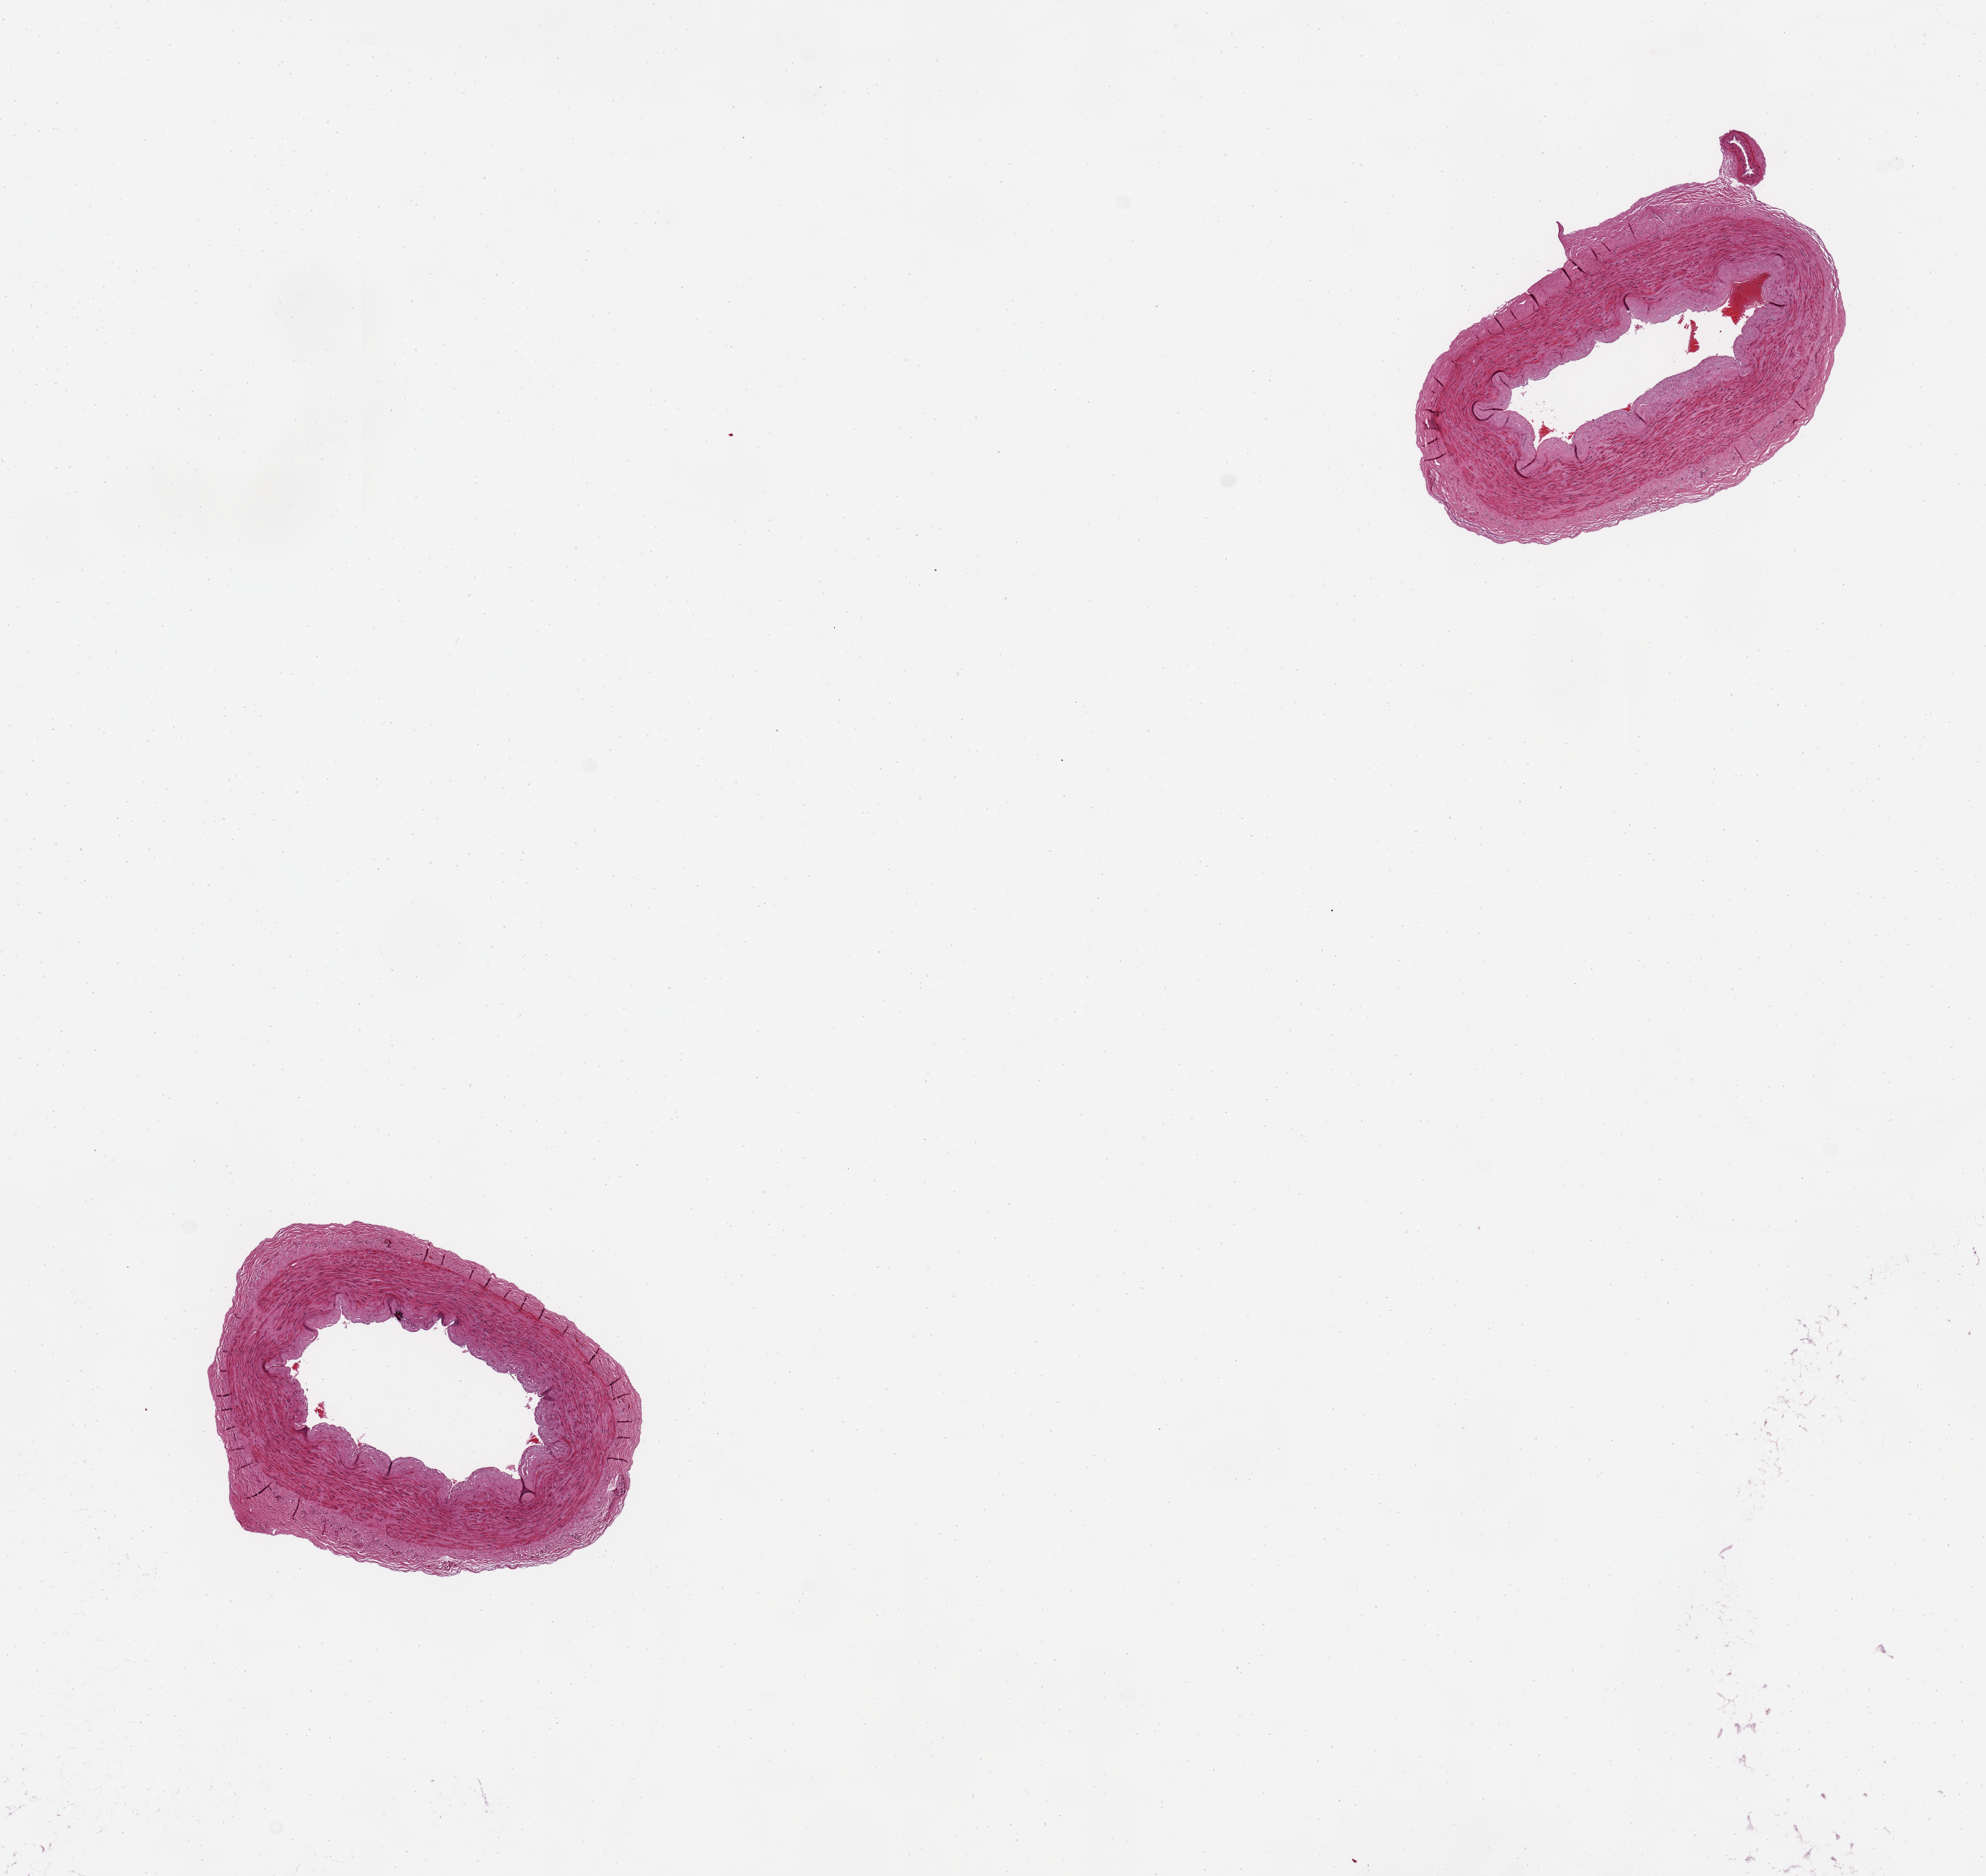
Whole-slide image, haematoxylin and eosin stain, brightfield, low-resolution overview of the scanned area, about 10.8 x 10.2 mm; PAXgene-fixed paraffin-embedded (PFPE) section; section of tibial artery (target tissue); tissue donor sample.
Reviewer comment on this tissue sample: 2 aliquoqts, ~2.5mm. Good clean speimens.